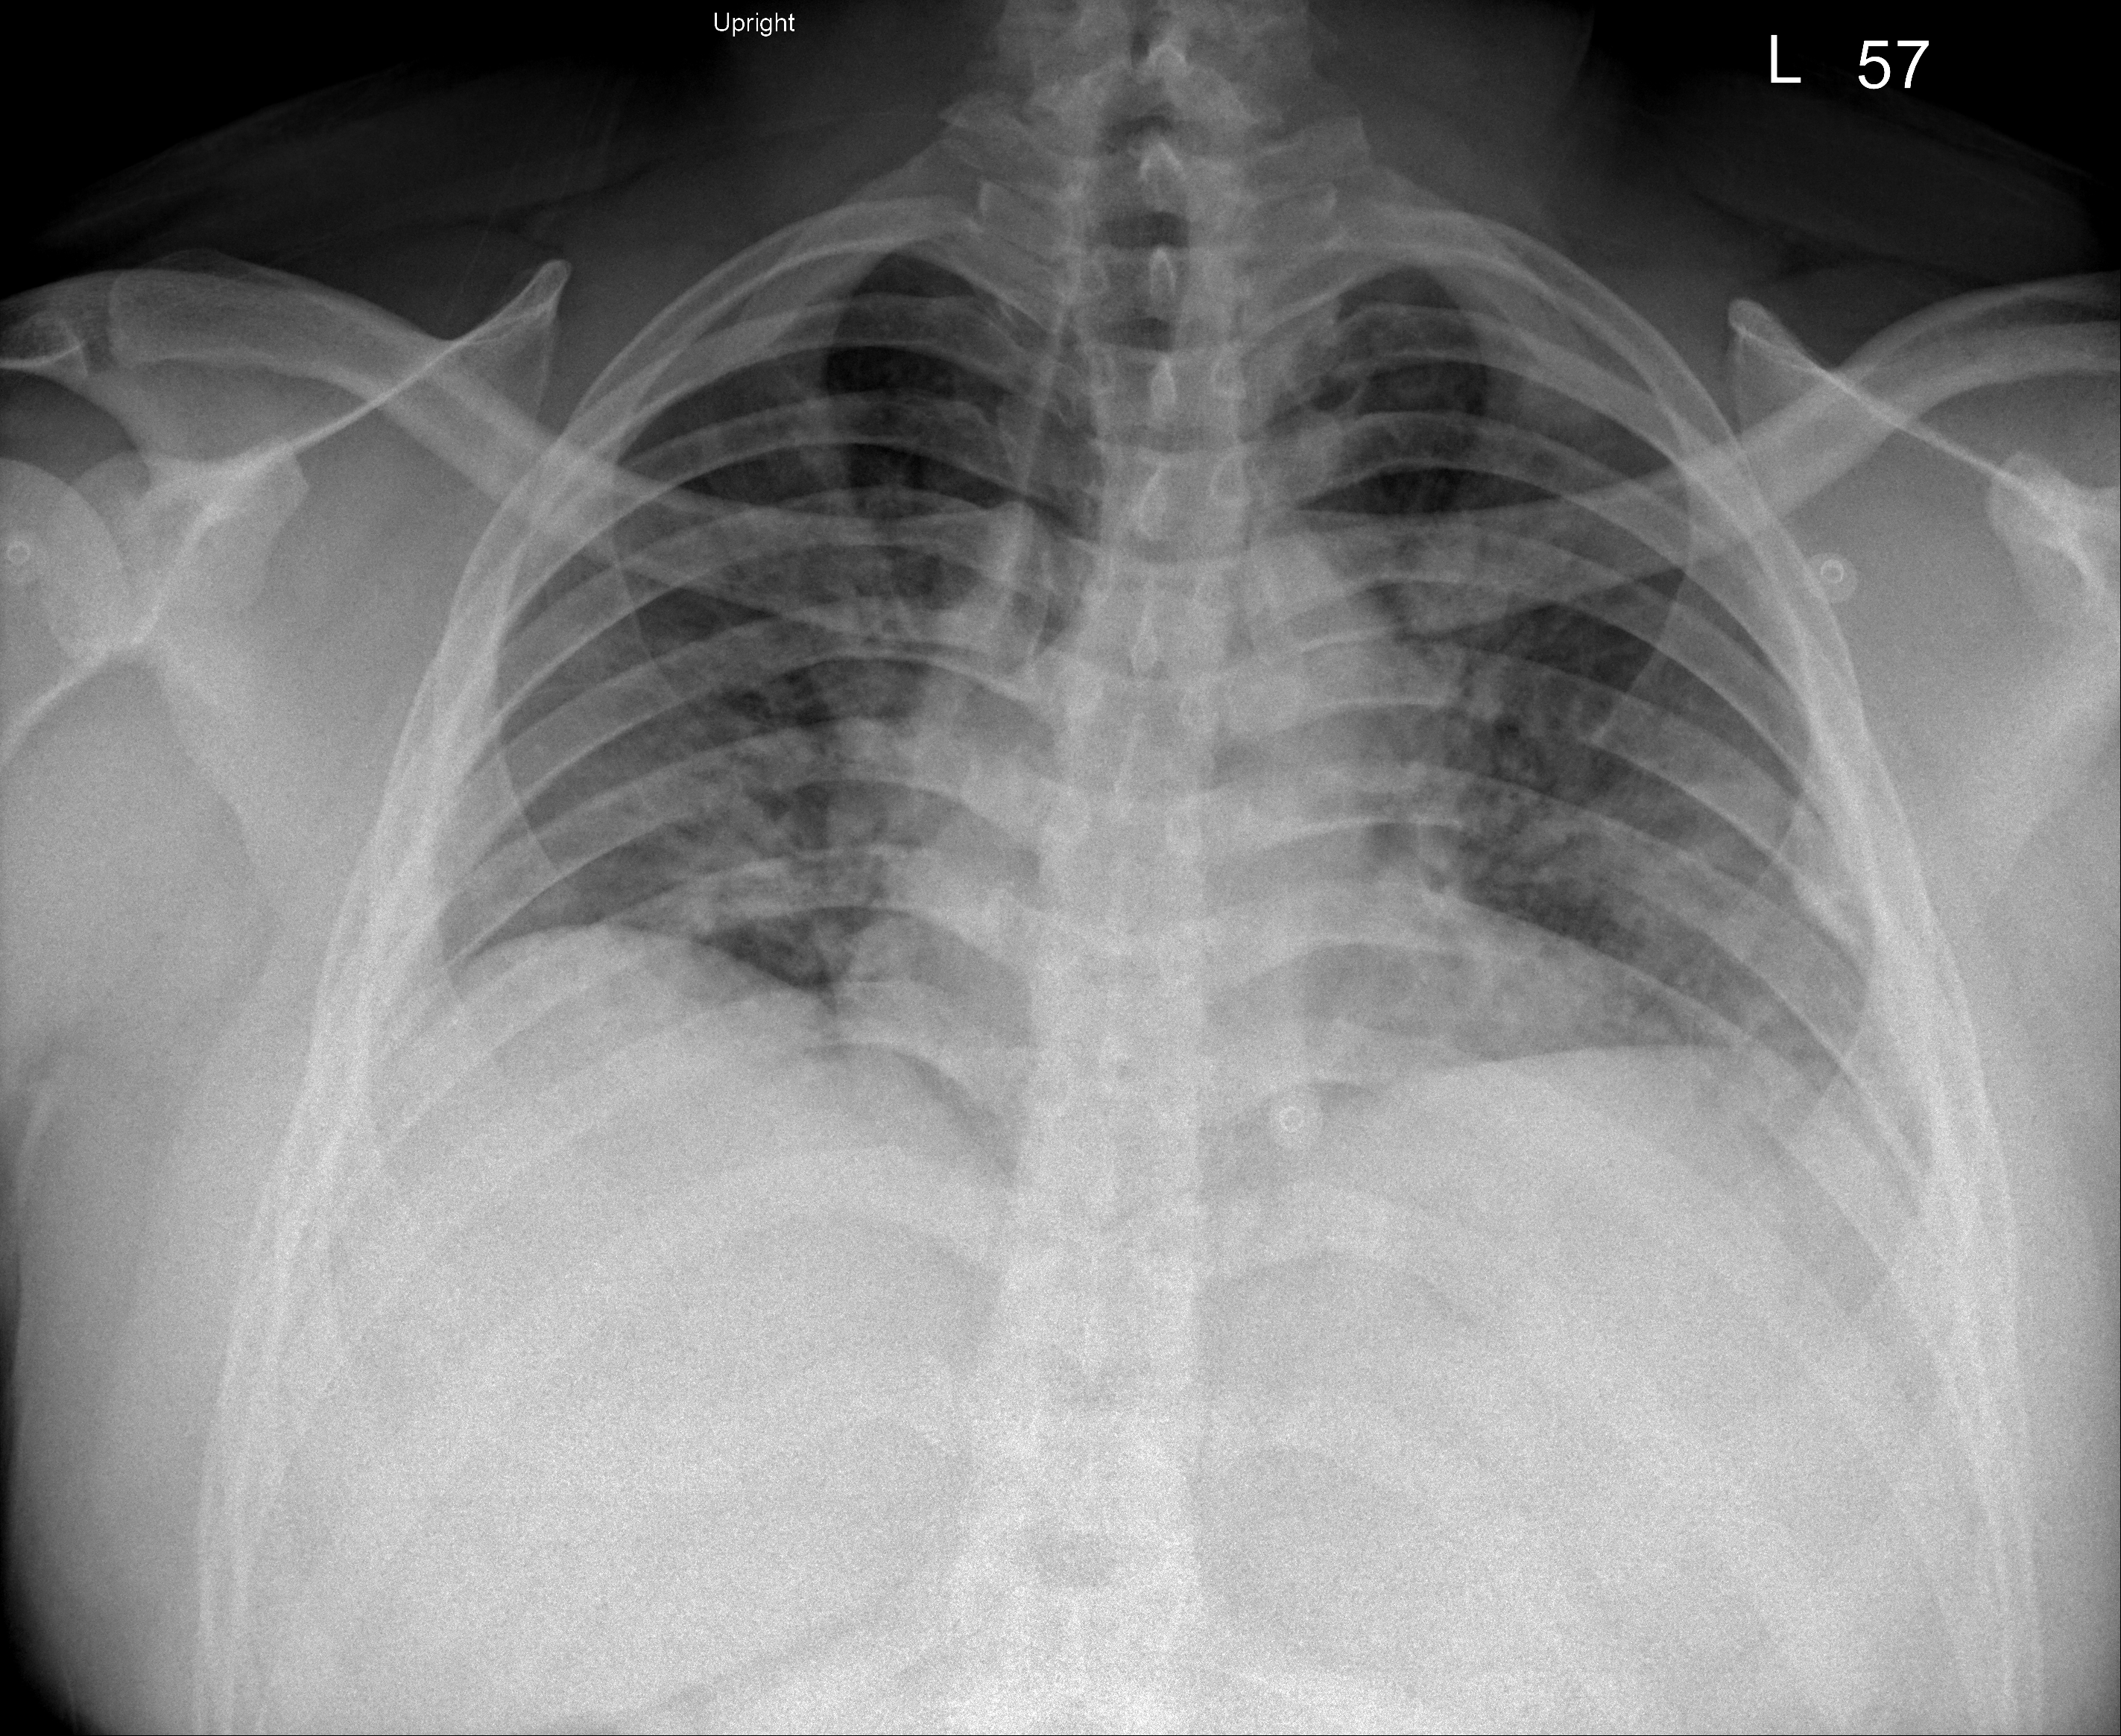
Chest X-ray (portable), AP projection. Male patient, age 36 years; COVID-19 (test-positive).
Radiologist's key findings for this exam: bilateral lower lung atelectatic changes and mild superimposed bilateral lower lung ill-defined airspace opacities are not significantly changed.